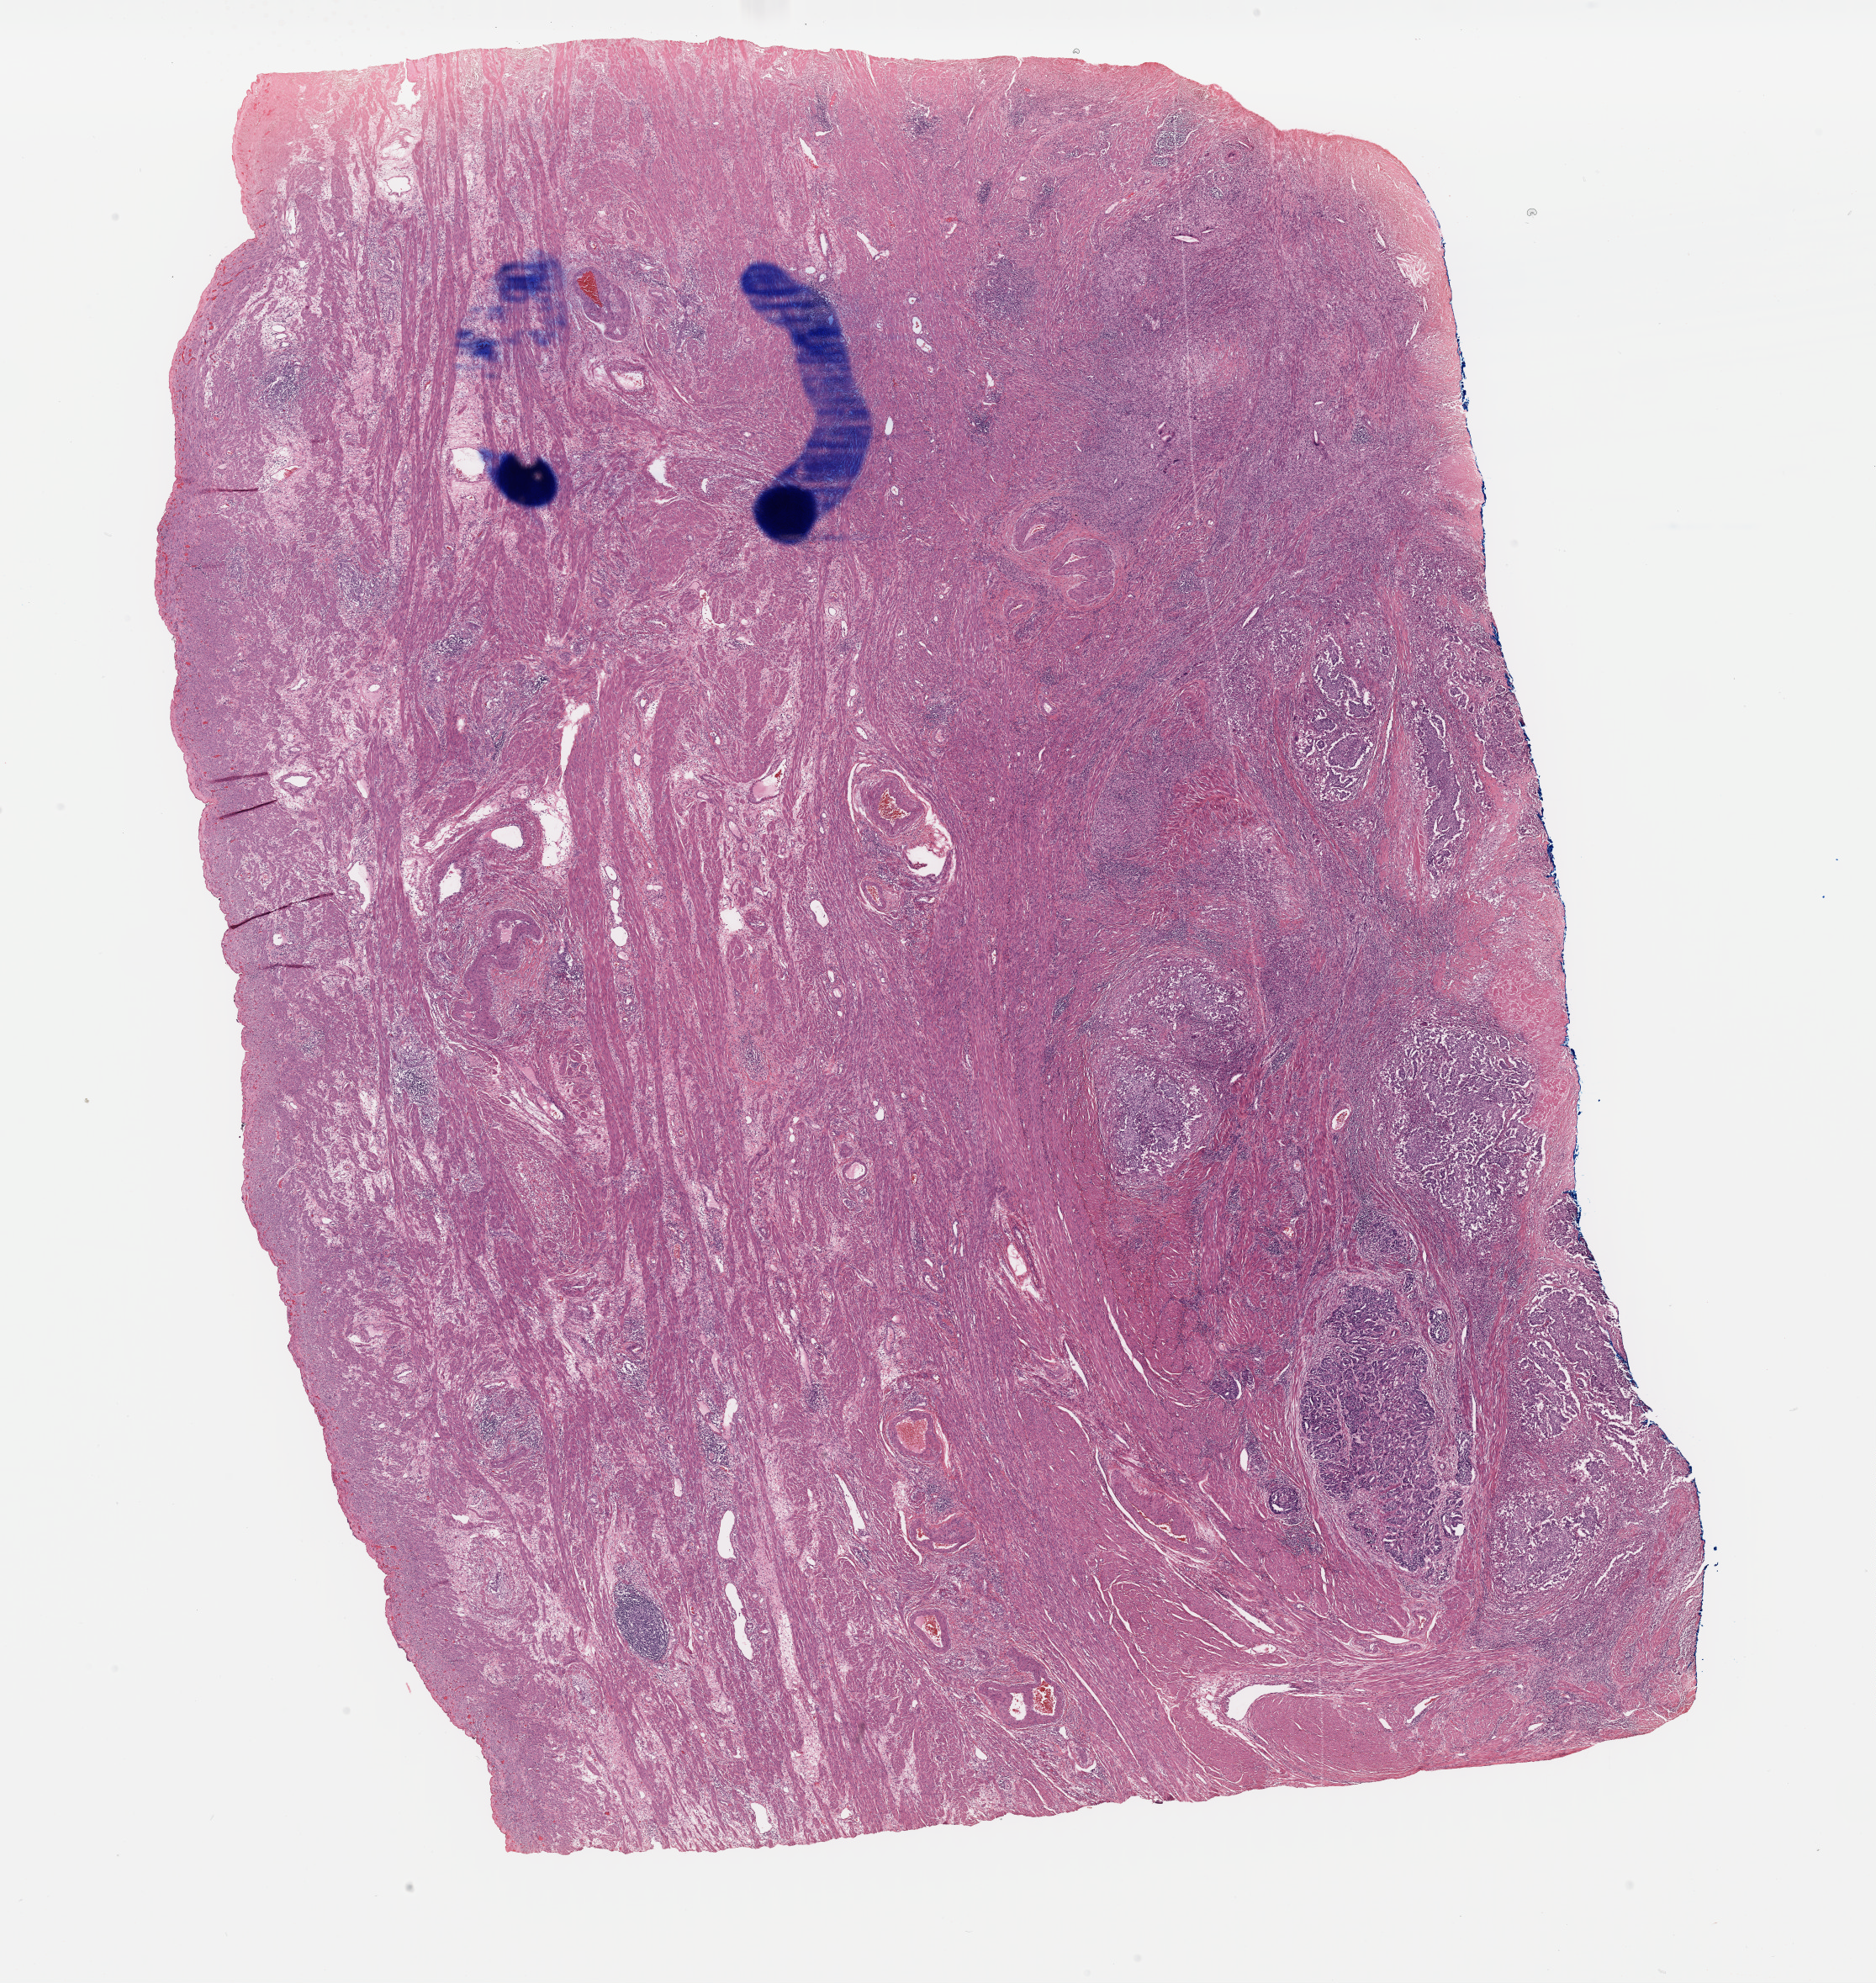
Digitized H&E tissue section (whole slide) — shown as a low-resolution overview of the whole scanned area (about 17.6 x 18.6 mm), formalin-fixed paraffin-embedded (FFPE) diagnostic section, primary tumour sample from the uterus. Female patient; age at initial diagnosis 59 years. Histologic grade: G3 (poorly differentiated).
FIGO stage: IVA. Lymph nodes positive (case pathology): 2 of 16 examined. Histologic diagnosis: Endometrioid adenocarcinoma, NOS.